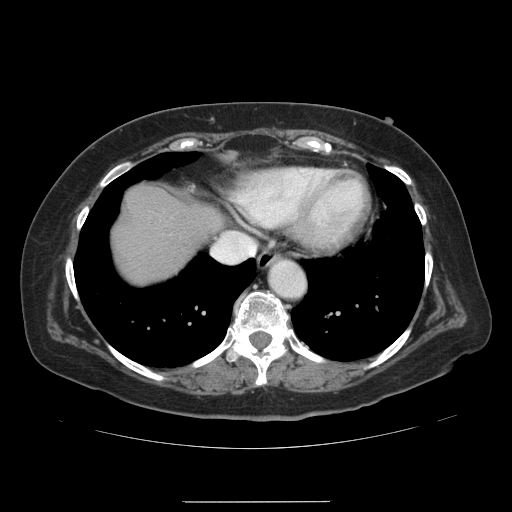
Contrast-enhanced abdominal CT, one axial slice; slice 124 of 141 in the series (ordered by position); intravenous contrast given; soft-tissue window (W 400 / L 40 HU); 2.5 mm slice thickness; 512 × 512 image matrix, field of view 393 × 393 mm. Female patient, age 74 years. Case-level facts recorded for this patient, not image findings: diagnosis: colorectal cancer liver metastases, imaged before liver resection; multiple liver metastases: yes; largest metastasis: 7 cm; disease in both lobes: yes.
Outlined on this slice (manually delineated by an expert):
- liver: bounding box <113,188,221,284> (left, top, right, bottom; pixels)
- planned liver remnant (the part of the liver to remain after resection): <113,188,221,284>